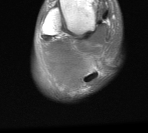
MRI of an extremity soft-tissue mass, one axial slice; position 9 of 76 along the scan axis; MR volume resampled by the dataset authors to the PET/CT grid (not the native acquisition matrix); 3.27 mm slice thickness; 148 × 133 image matrix. Male patient. Case-level facts recorded for this patient, not image findings: histological type: liposarcoma - round cell; grade: high; site of the primary tumour: right calf.
Structures marked on this image (expert contour drawn on MRI and transferred to this co-registered scan by the dataset authors):
- gross tumour volume (mass): bounding box <38,35,110,93> (left, top, right, bottom; pixels)